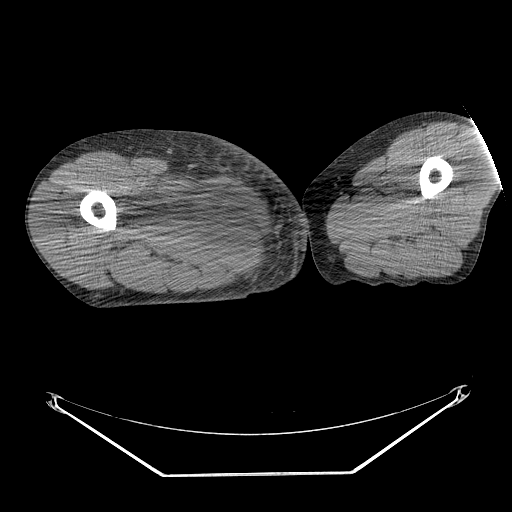
CT of an extremity soft-tissue mass (from a PET/CT study), one axial slice. Slice 243 of 311 in the series (ordered by position). 140 kVp. Soft-tissue window (W 400 / L 40 HU). 512 × 512 image matrix, field of view 500 × 500 mm. Male patient. From the clinical record (not read from this slice): histological type: undifferentiated - pleiomorphic; grade: high; site of the primary tumour: right thigh.
Outlined on this slice (expert contour drawn on MRI and transferred to this co-registered scan by the dataset authors):
- gross tumour volume including surrounding oedema: bounding box (x1, y1, x2, y2) in pixels: (128, 177, 225, 248)
- gross tumour volume (mass): (164, 185, 225, 245)